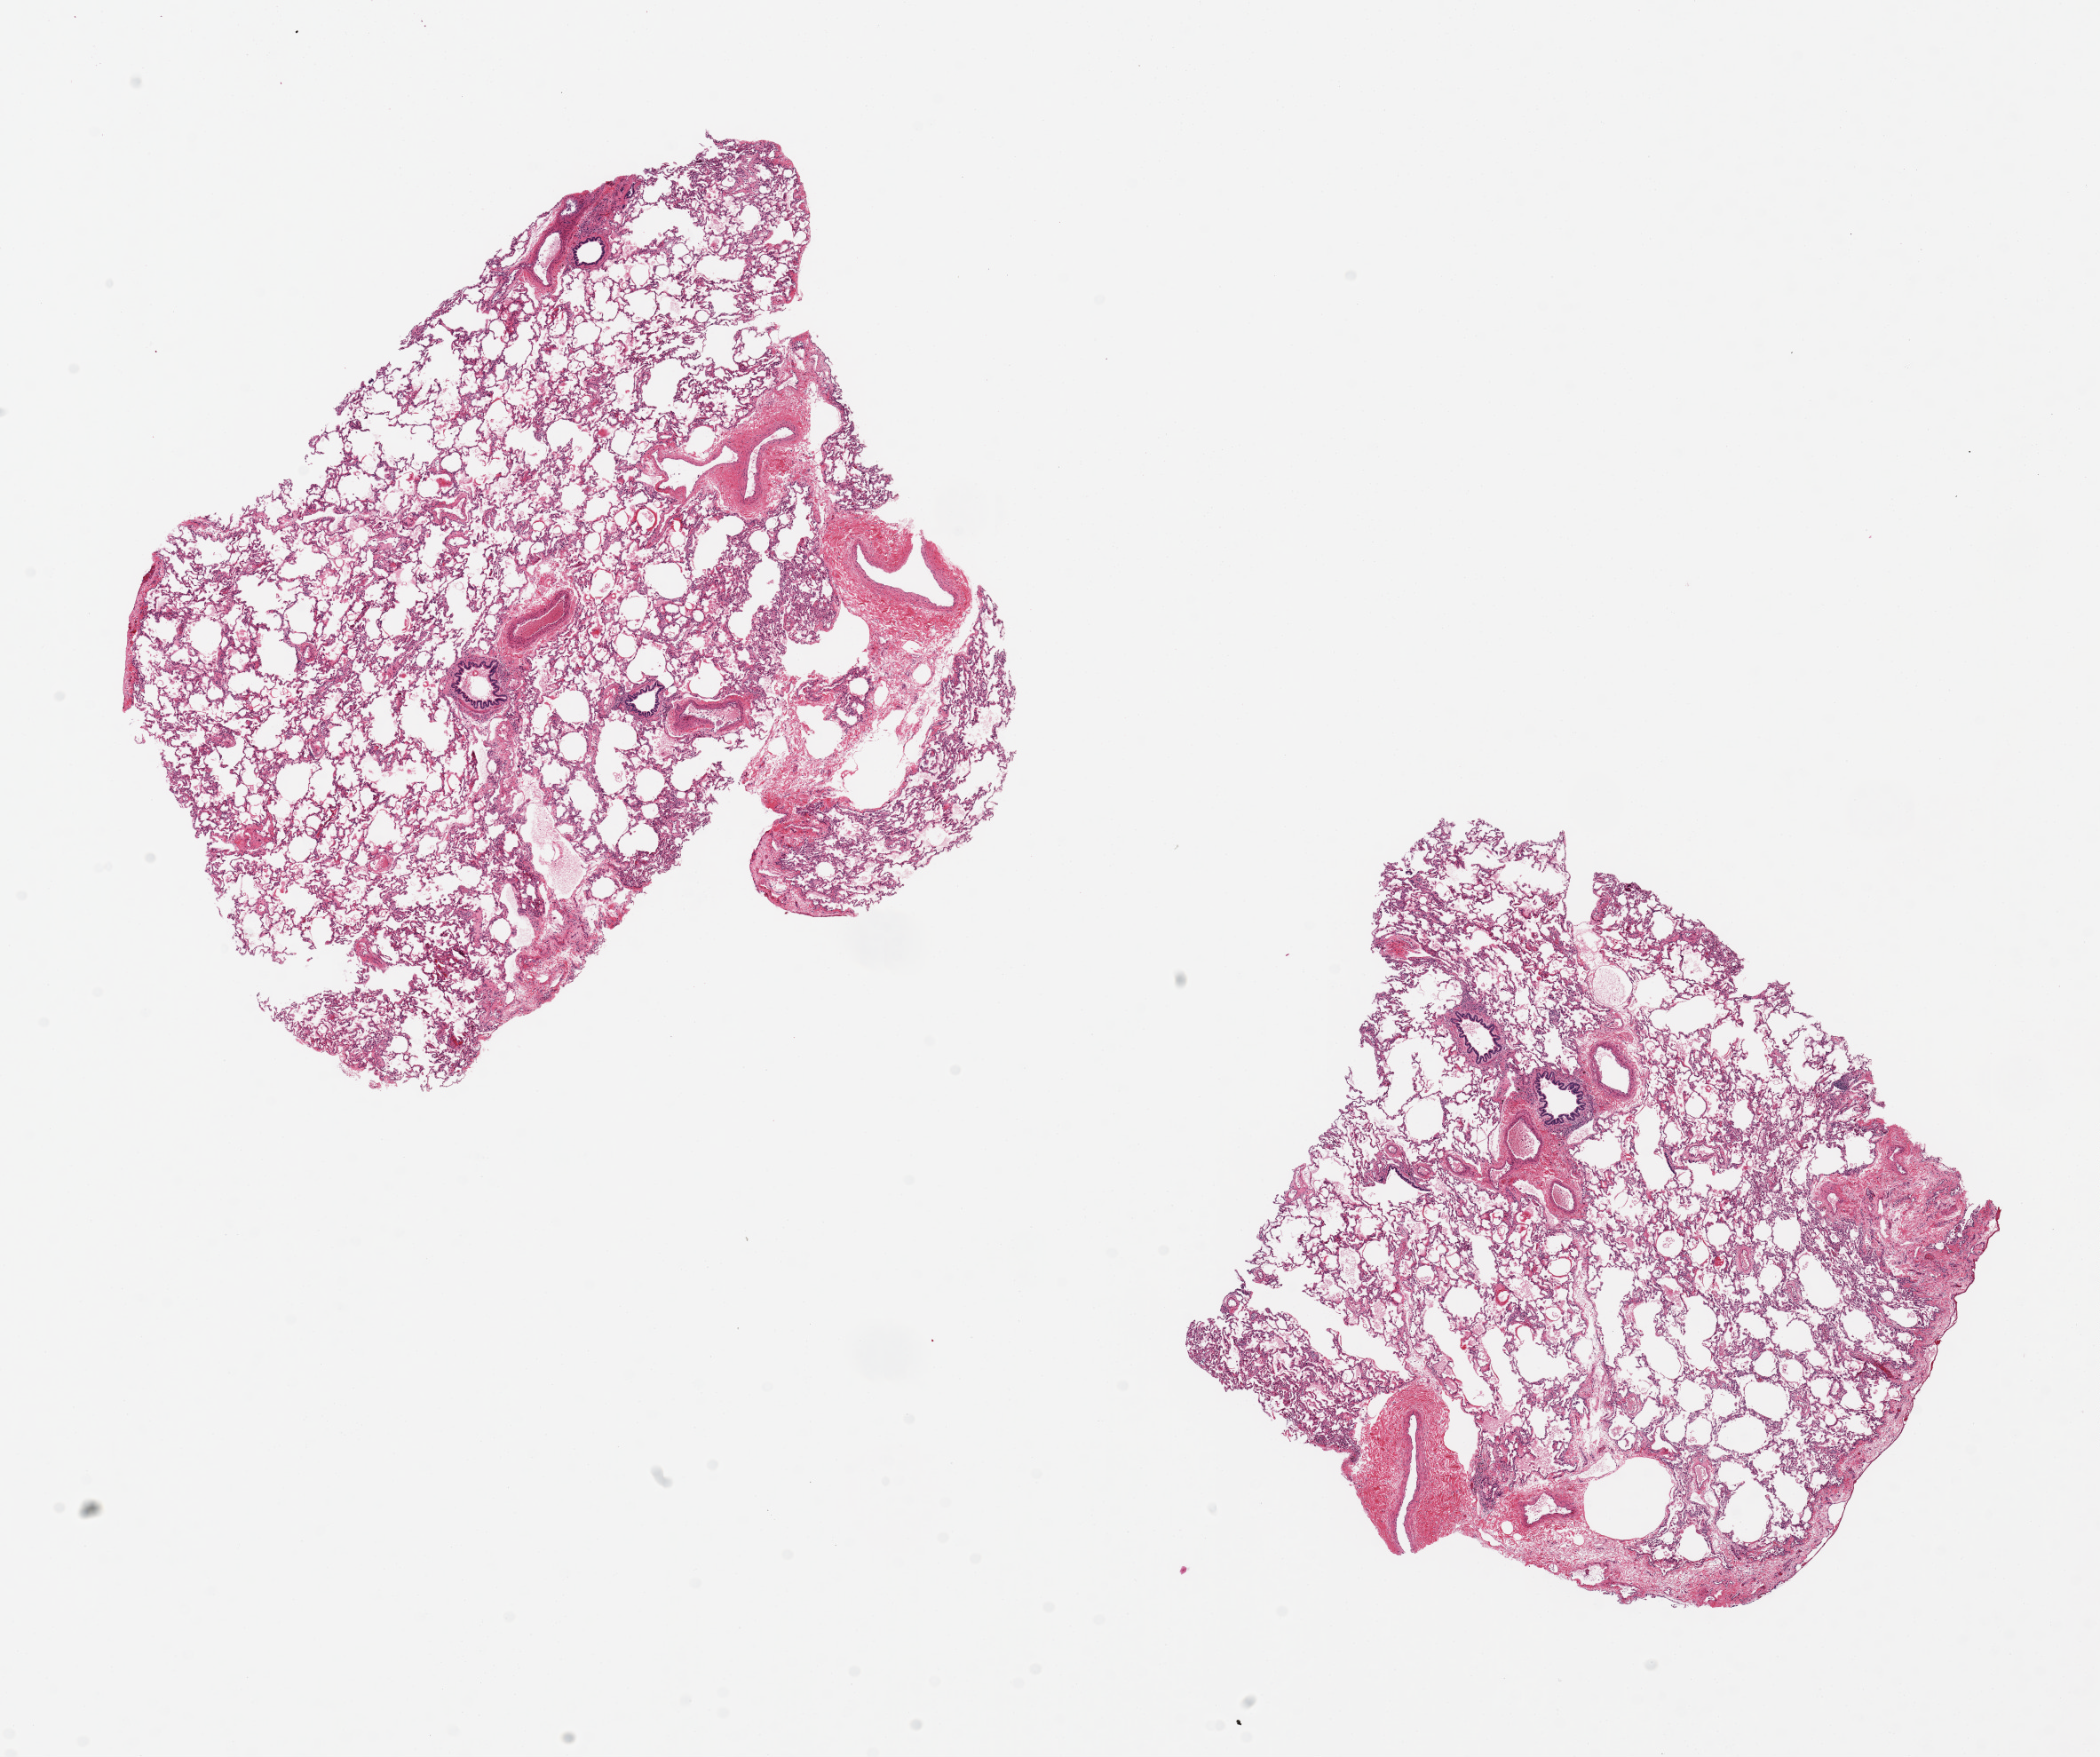
Haematoxylin and eosin whole-slide image, brightfield, low-resolution overview of the scanned area, about 18.7 x 15.7 mm; PAXgene-fixed paraffin-embedded (PFPE) section; target tissue: lung; donor tissue sample. Male donor.
Reviewer comment on this tissue sample: 2 pieces ~7x6mm; Well preserved, mild emphysematous changes; Good bronchial preservation, representative bronchioles.